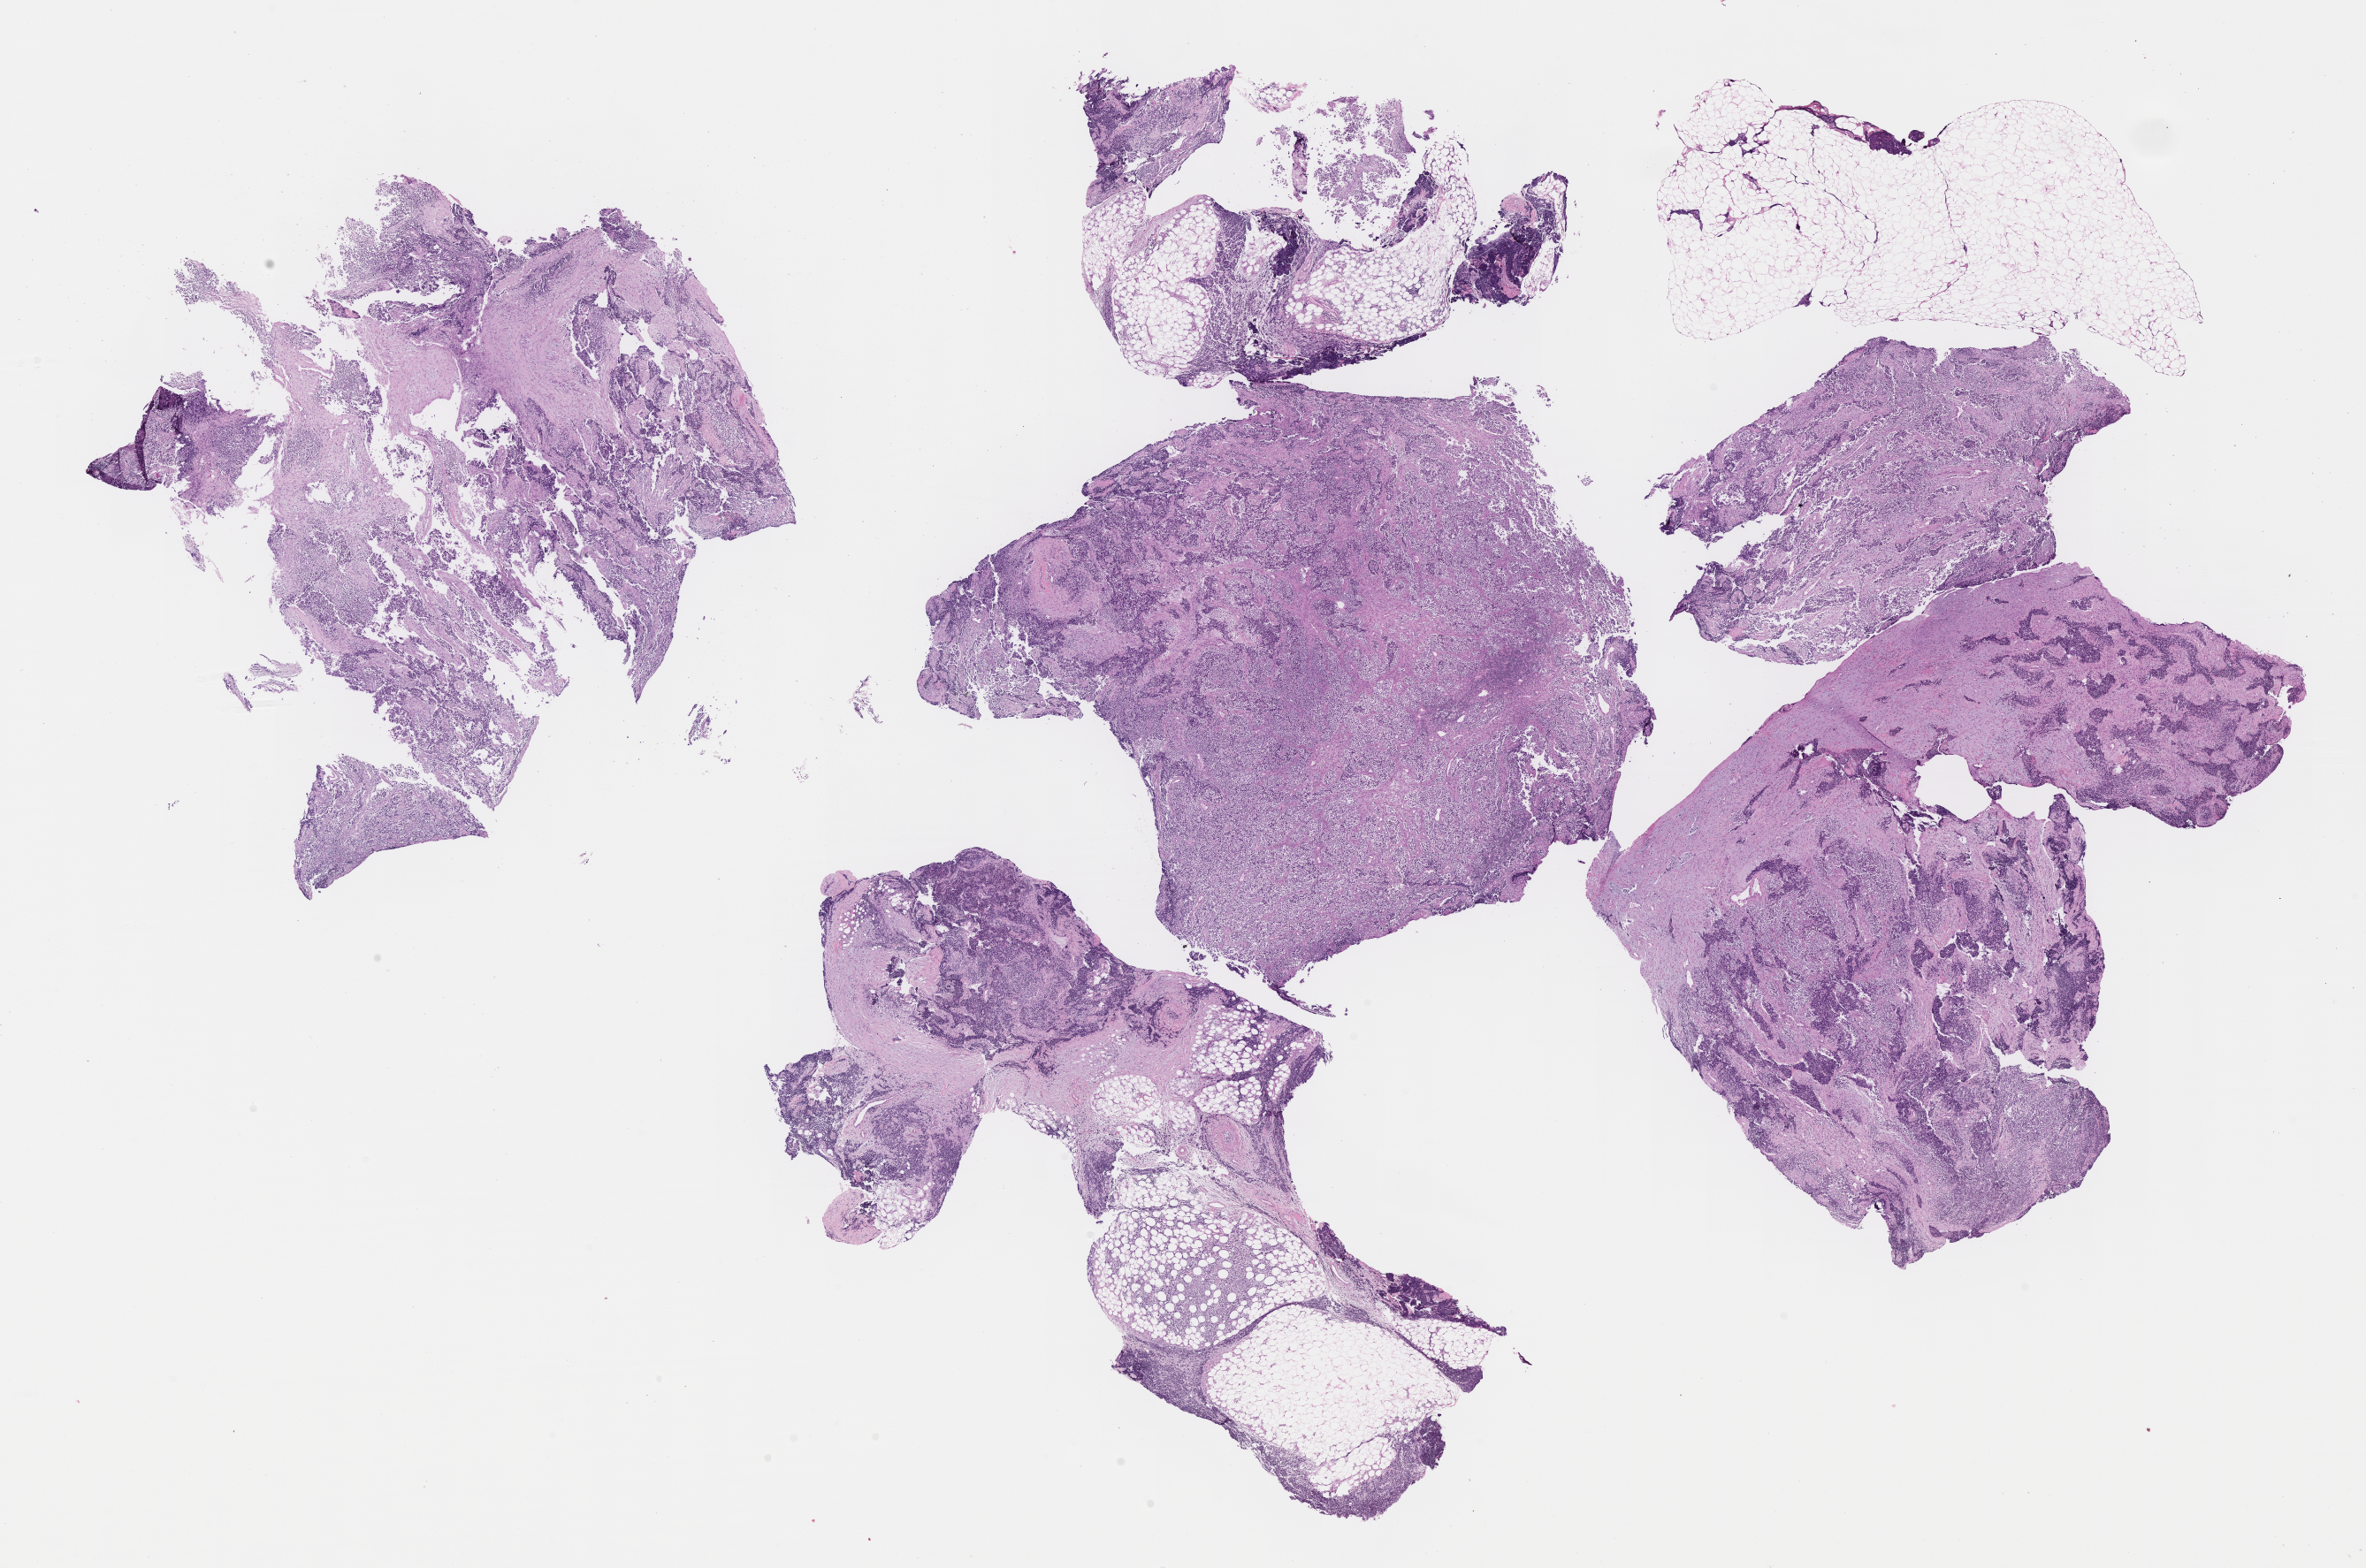
H&E whole-slide image of tumor tissue, shown as a low-resolution overview of the whole scanned area (about 21.6 x 14.3 mm); formalin-fixed paraffin-embedded section; sample anatomic site: right inguinal. Patient: male, age 1.1 years at diagnosis.
Diagnosis: rhabdomyosarcoma; histological classification: embryonal rhabdomyosarcoma. Stage (as recorded): 4.